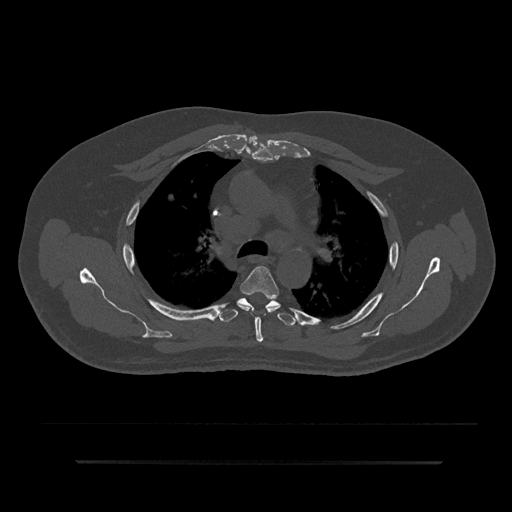
CT including the spine, one axial slice; slice 601 of 797 in the series (ordered by position); bone window (W 1800 / L 400 HU); 0.5 mm slice thickness; 512 × 512 image matrix, field of view 464 × 464 mm. Male patient, age 59 years. Case-level facts recorded for this patient, not image findings: primary cancer: bile ducts.
Structures marked on this image (semi-automatic segmentation, software-assisted and operator-edited):
- T4 vertebra: bounding box [x1, y1, x2, y2] px = [239, 266, 280, 343]
- T5 vertebra: [219, 297, 298, 326]